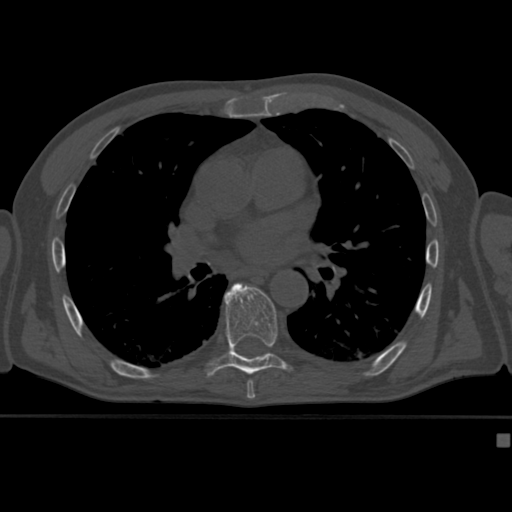
CT including the spine, one axial slice. Slice 265 of 430 in the series (ordered by position). 120 kVp. Bone window (W 1800 / L 400 HU). 512 × 512 image matrix, field of view 337 × 337 mm. Male patient, age 64 years. Case-level facts recorded for this patient, not image findings: primary cancer: uterus; vertebrae with lytic lesions (as recorded): T1, T4, T5, T7, L5.
Structures marked on this image (semi-automatic segmentation, software-assisted and operator-edited):
- T7 vertebra: bounding box (x1, y1, x2, y2) in pixels: (248, 379, 253, 382)
- T8 vertebra: (205, 282, 292, 377)